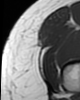
MRI of an extremity soft-tissue mass, one axial slice; position 9 of 46 along the scan axis; MR volume resampled by the dataset authors to the PET/CT grid (not the native acquisition matrix); 3.27 mm slice thickness; 80 × 100 image matrix, field of view 78 × 98 mm. Female patient. Case-level facts recorded for this patient, not image findings: histological type: synovial sarcoma; grade: intermediate; site of the primary tumour: right thigh.
Annotated regions visible in this slice (expert contour drawn on MRI and transferred to this co-registered scan by the dataset authors):
- gross tumour volume including surrounding oedema: box from (x=39, y=35) to (x=45, y=45) px
- gross tumour volume (mass): (x=37, y=35)–(x=45, y=45)